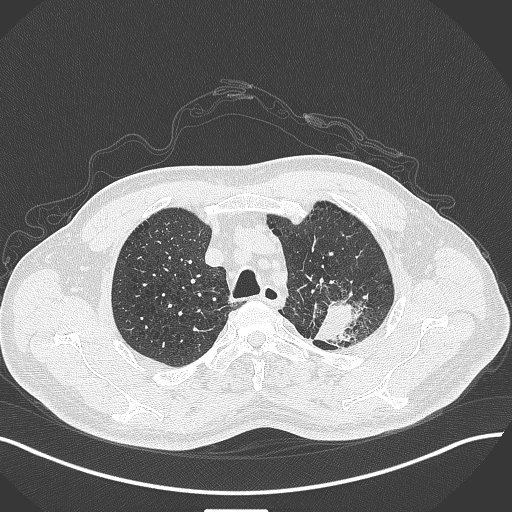
Chest CT, one axial slice; slice 345 of 429 in the series (ordered by position); reconstruction kernel B70f; 120 kVp; lung window (W 1500 / L -600 HU); 1 mm slice thickness; 512 × 512 image matrix. Patient: male, 55 years. Case-level facts recorded for this patient, not image findings: clinical TNM (as recorded): T3 N0 M1c.
Annotated regions visible in this slice (rectangle marked by the reading radiologist):
- lung tumour (recorded histology: adenocarcinoma): bounding box [x1, y1, x2, y2] px = [315, 295, 371, 350]